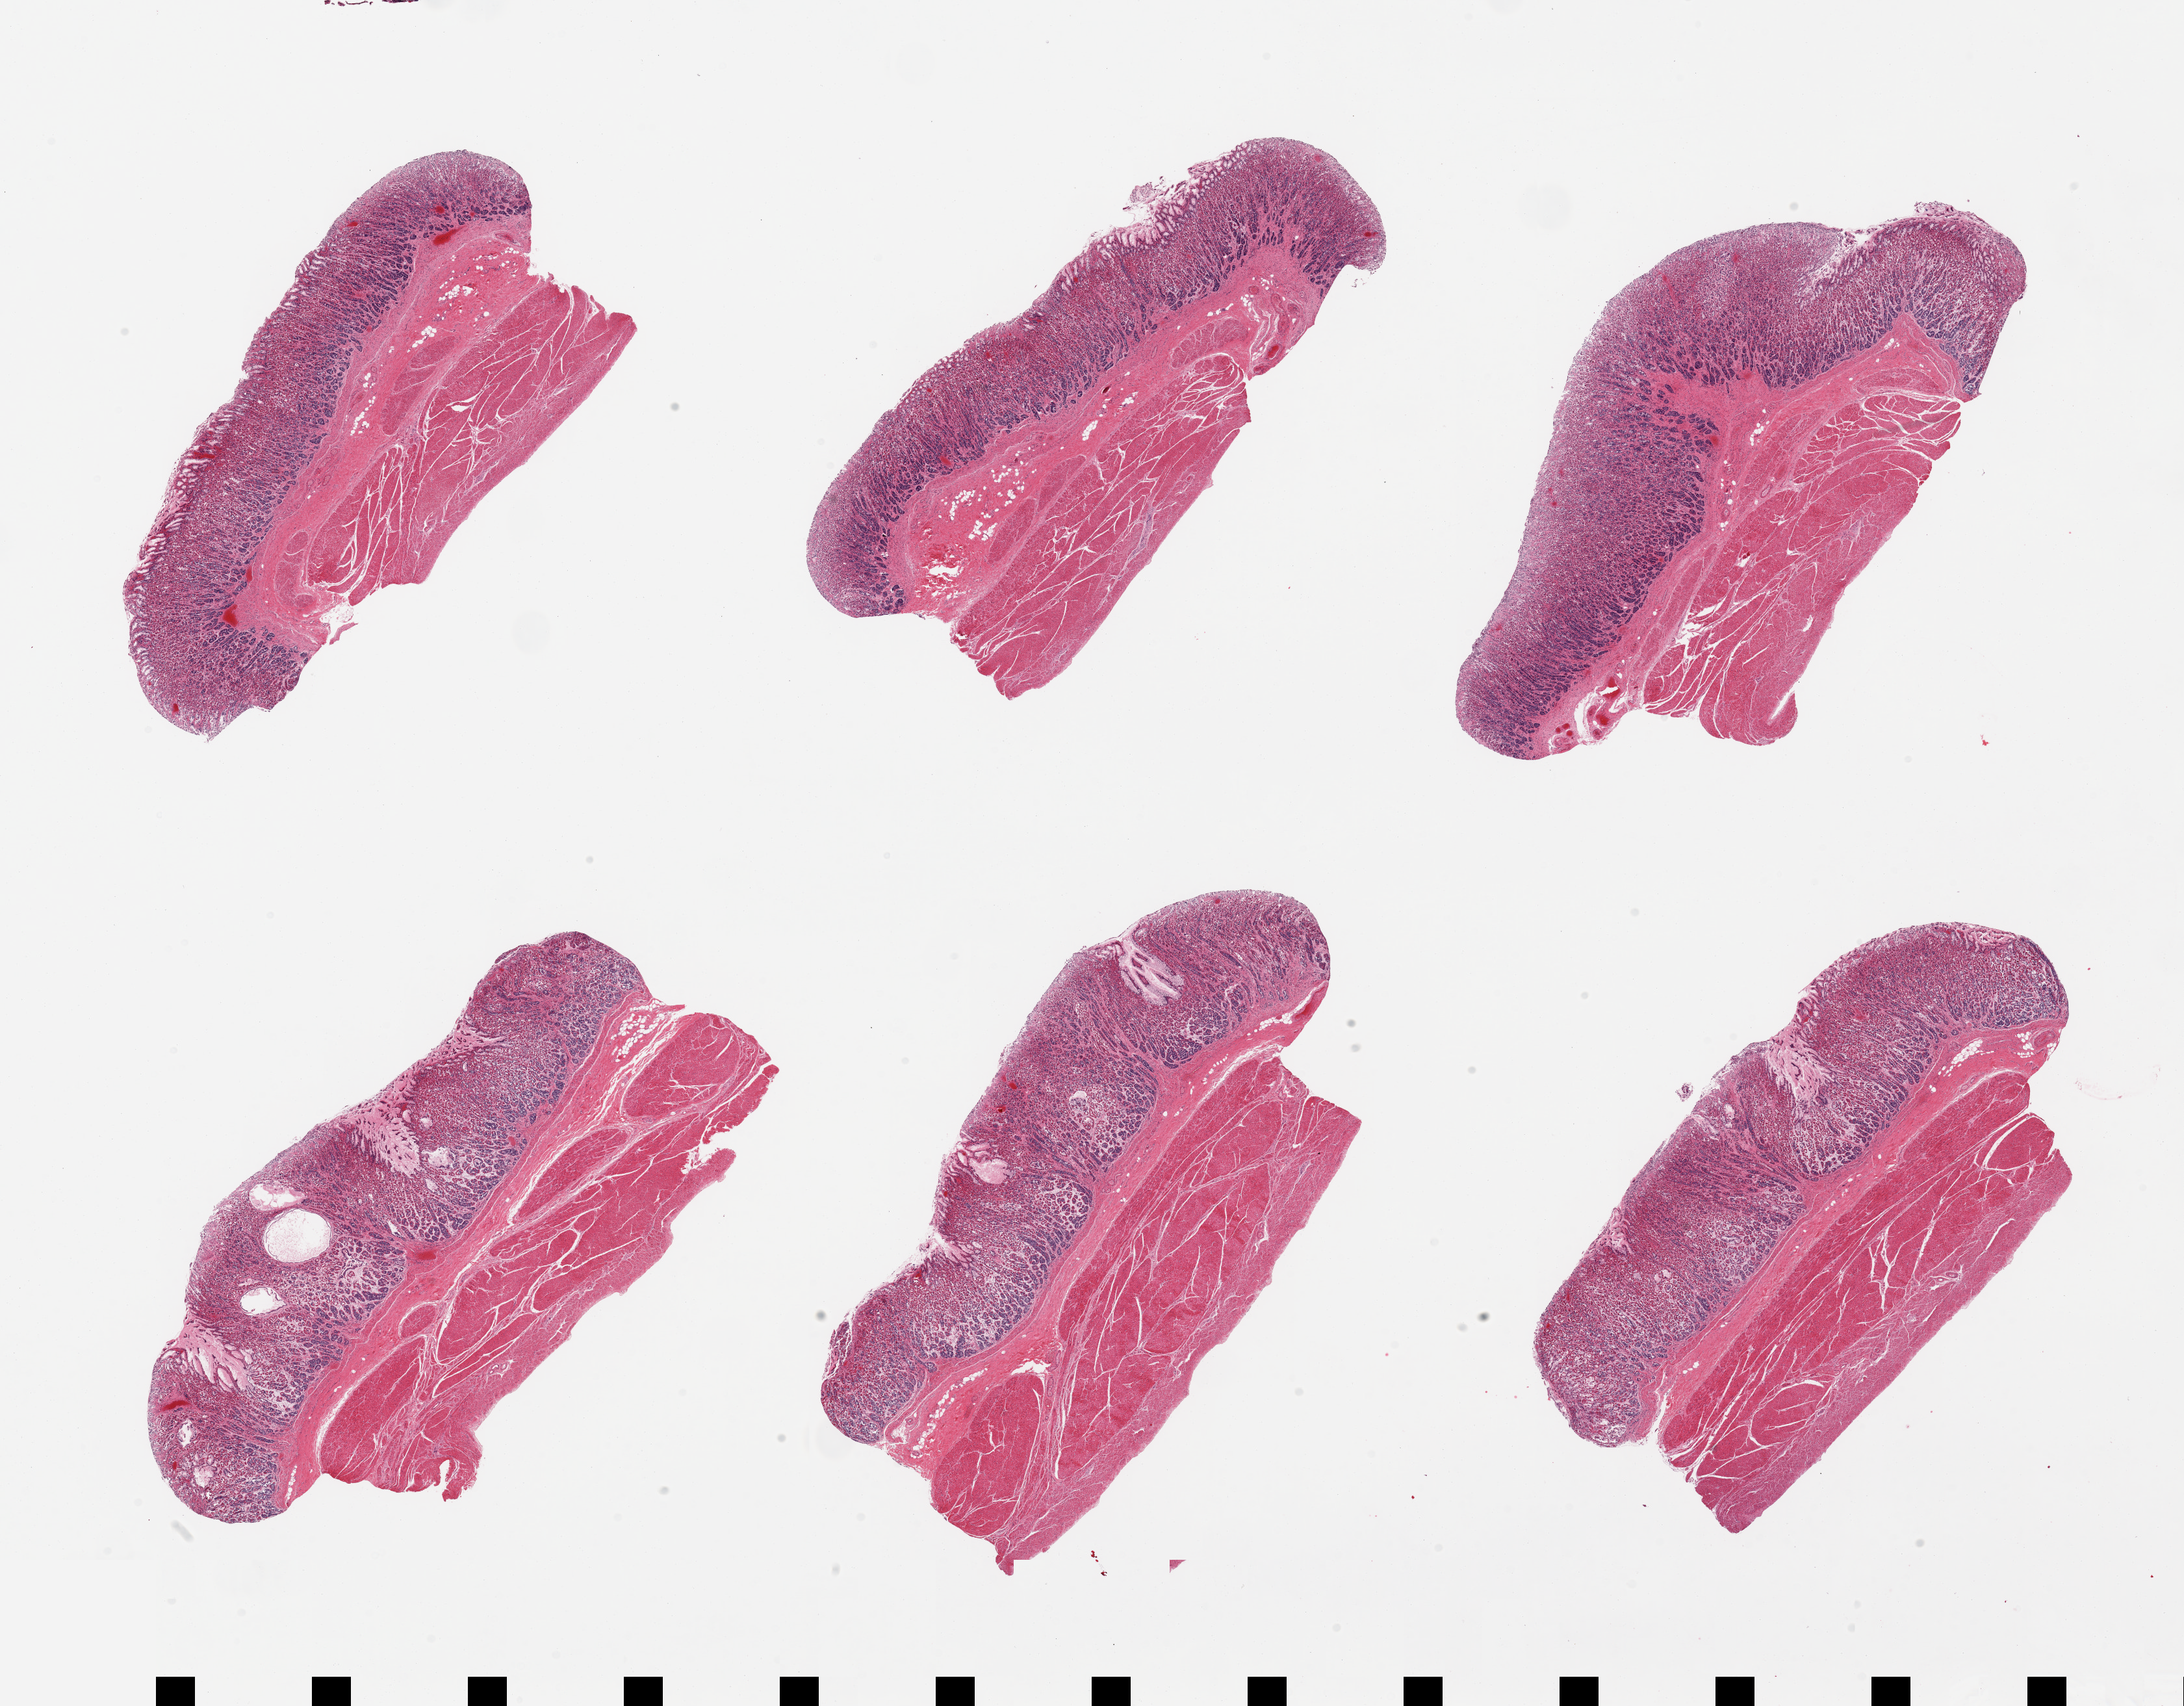
Whole-slide image, H&E stain — shown as a low-resolution overview of the whole scanned area (about 26.6 x 20.8 mm), PAXgene-fixed paraffin-embedded (PFPE) section, sampled site (target tissue): stomach, tissue donor sample. Male donor.
Pathologist's review note for this sample: 6 pieces, mucosa focally better preserved; gastropathic changes, up to ~2mm thick, 50-60% thickness.